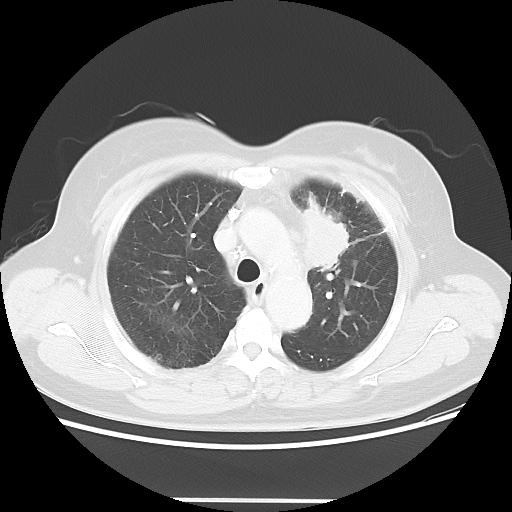
Chest CT, one axial slice. Slice 40 of 52 in the series (ordered by position). Reconstruction kernel LUNG. 120 kVp. Lung window (W 1500 / L -600 HU). 5 mm slice thickness. 512 × 512 image matrix. Patient: female, 52 years. Case-level facts recorded for this patient, not image findings: clinical TNM (as recorded): T2 N3 M0.
Annotated regions visible in this slice (rectangle marked by the reading radiologist):
- lung tumour (recorded histology: adenocarcinoma): bounding box [x1, y1, x2, y2] px = [290, 189, 351, 274]